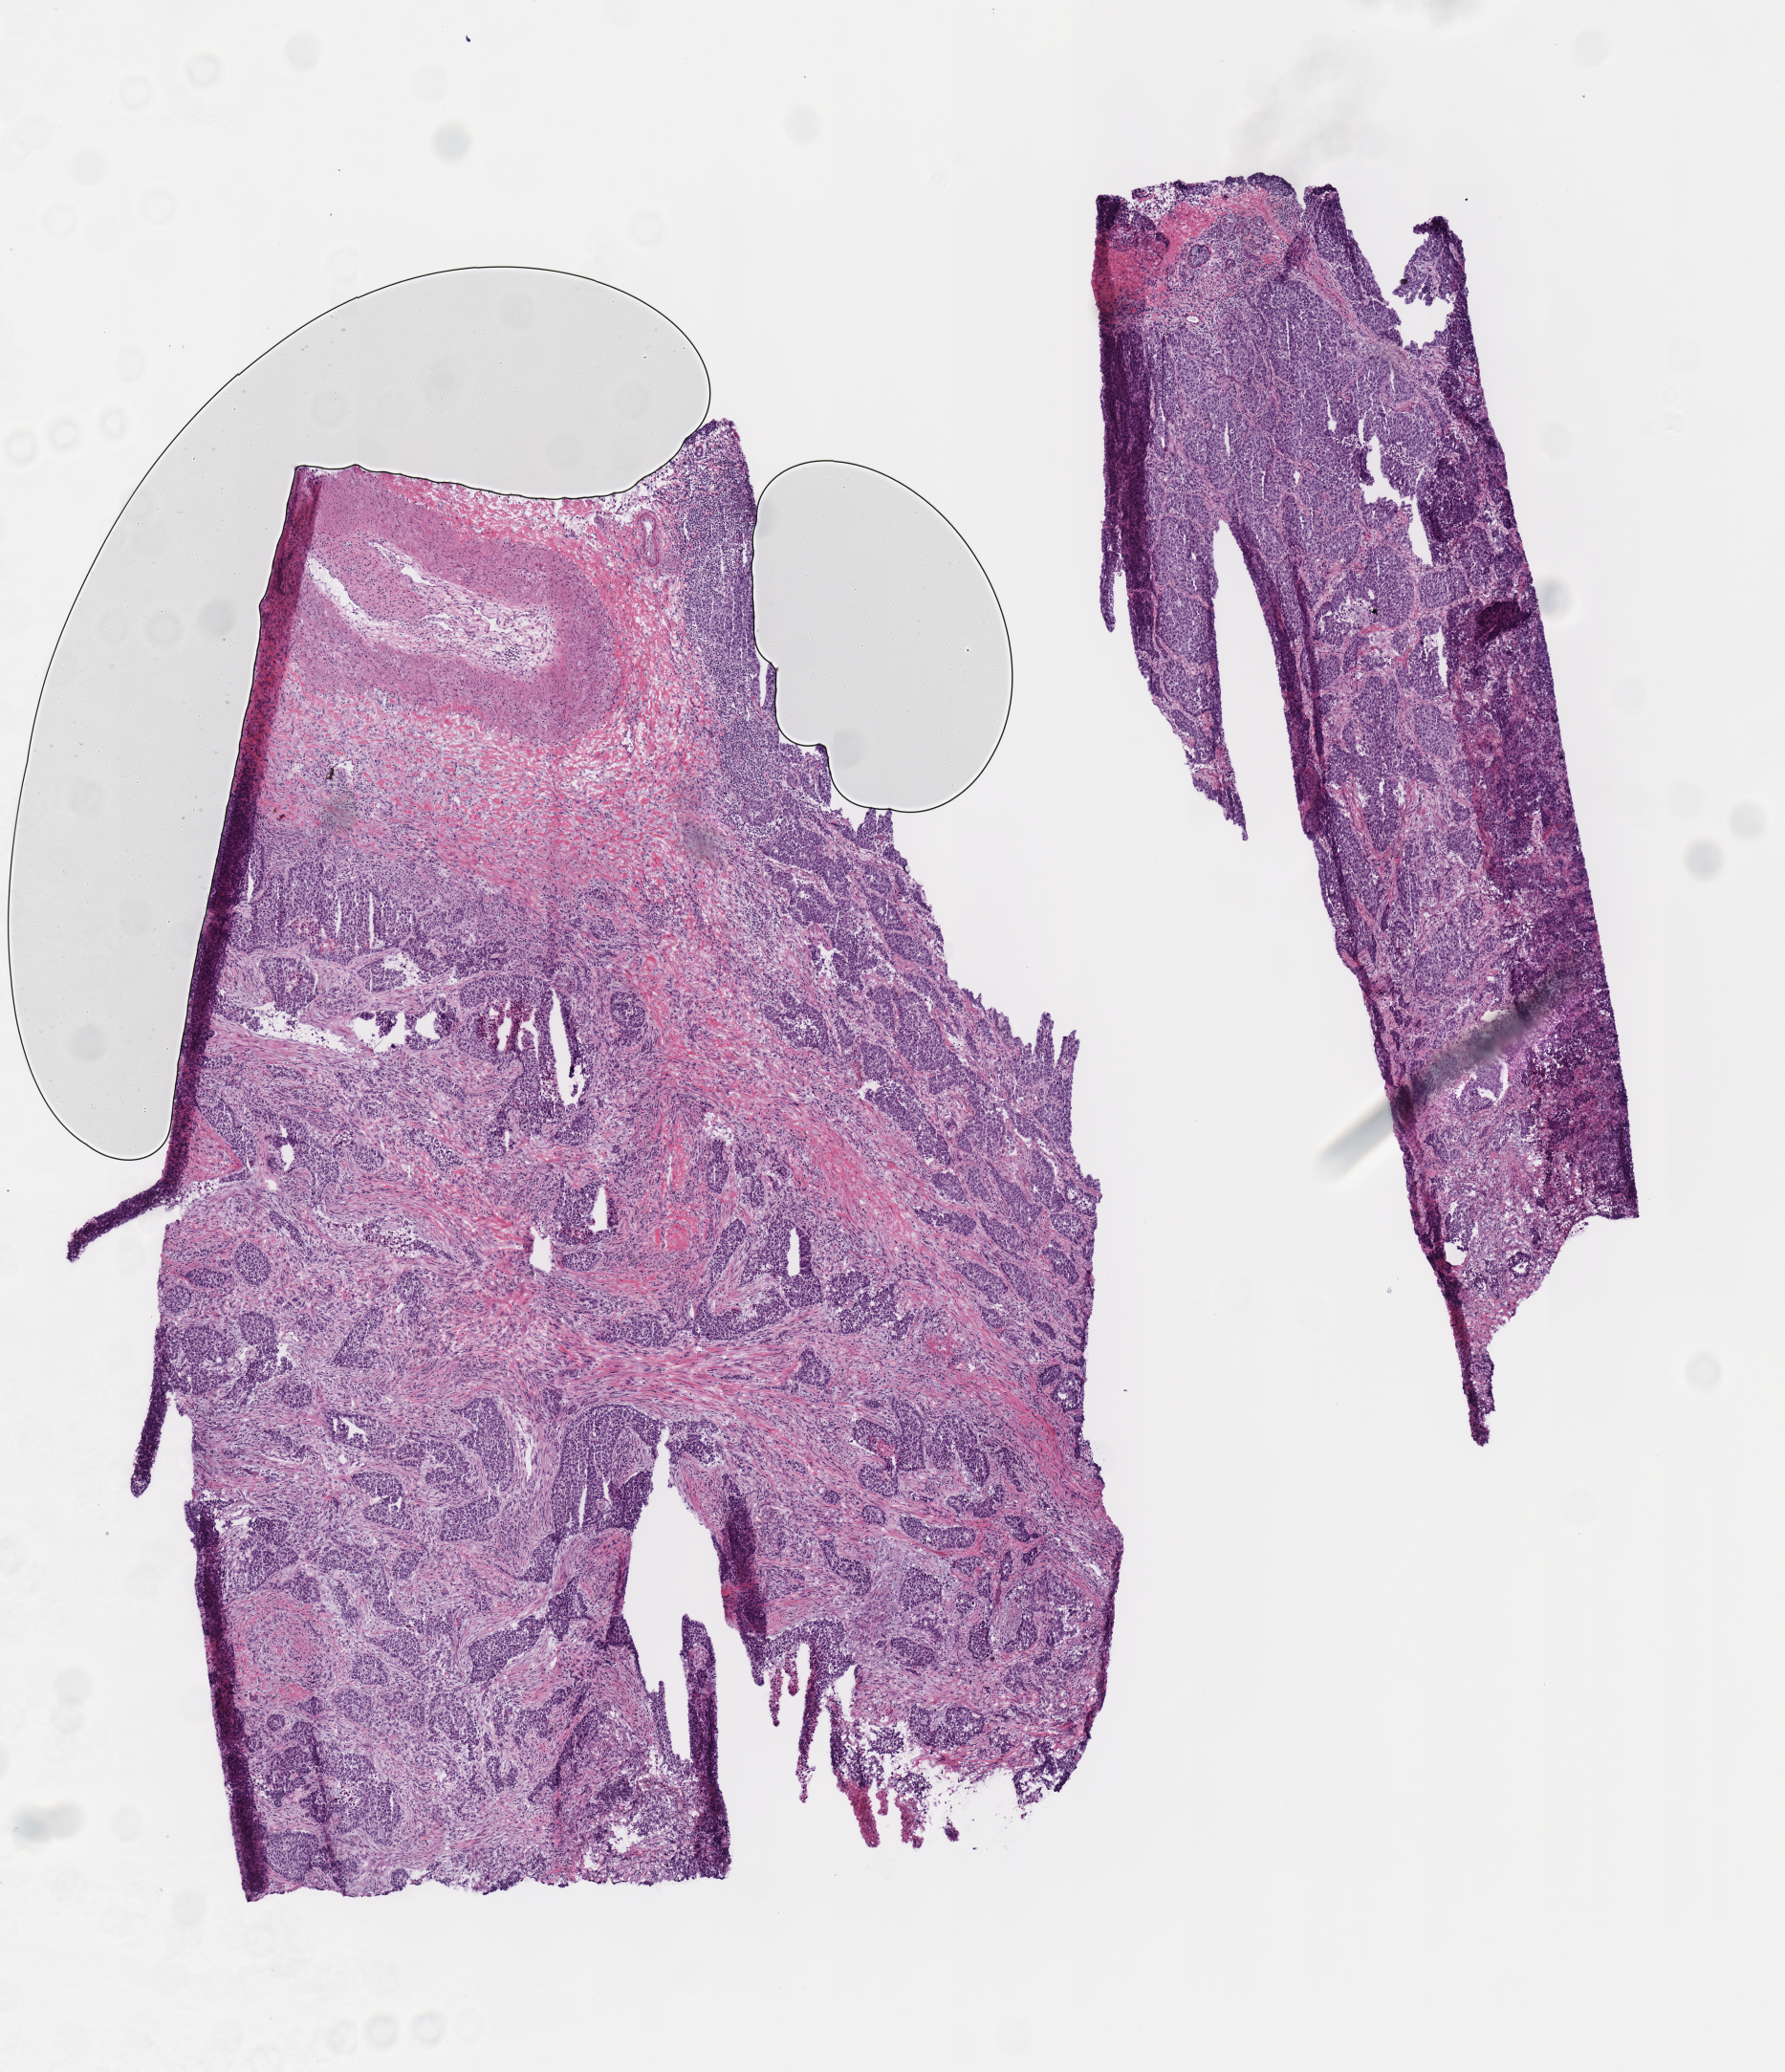
Whole-slide histology image, H&E, whole scanned area (about 7.3 x 8.5 mm) shown as a low-resolution overview, frozen section from the top of the tissue portion, sample: primary tumour, lung. Male, age 72 years at initial diagnosis. Composition of this section per pathologist review: tumour cells 80%, tumour nuclei 60%.
Diagnosis: Adenocarcinoma, NOS.